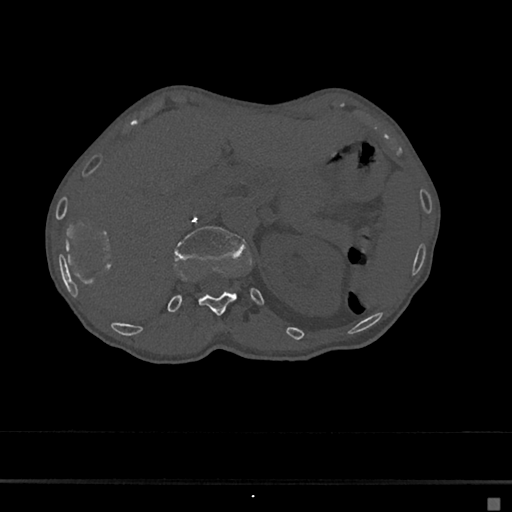
CT including the spine, one axial slice. Slice 112 of 797 in the series (ordered by position). Reconstruction kernel Br40s/3. 120 kVp. Bone window (W 1800 / L 400 HU). 0.5 mm slice thickness. 512 × 512 image matrix. Patient: female, 68 years. Case-level facts recorded for this patient, not image findings: primary cancer: renal.
Outlined on this slice (semi-automatically segmented with operator editing):
- L1 vertebra: bounding box [x1, y1, x2, y2] px = [174, 226, 248, 259]
- T12 vertebra: [197, 268, 237, 315]